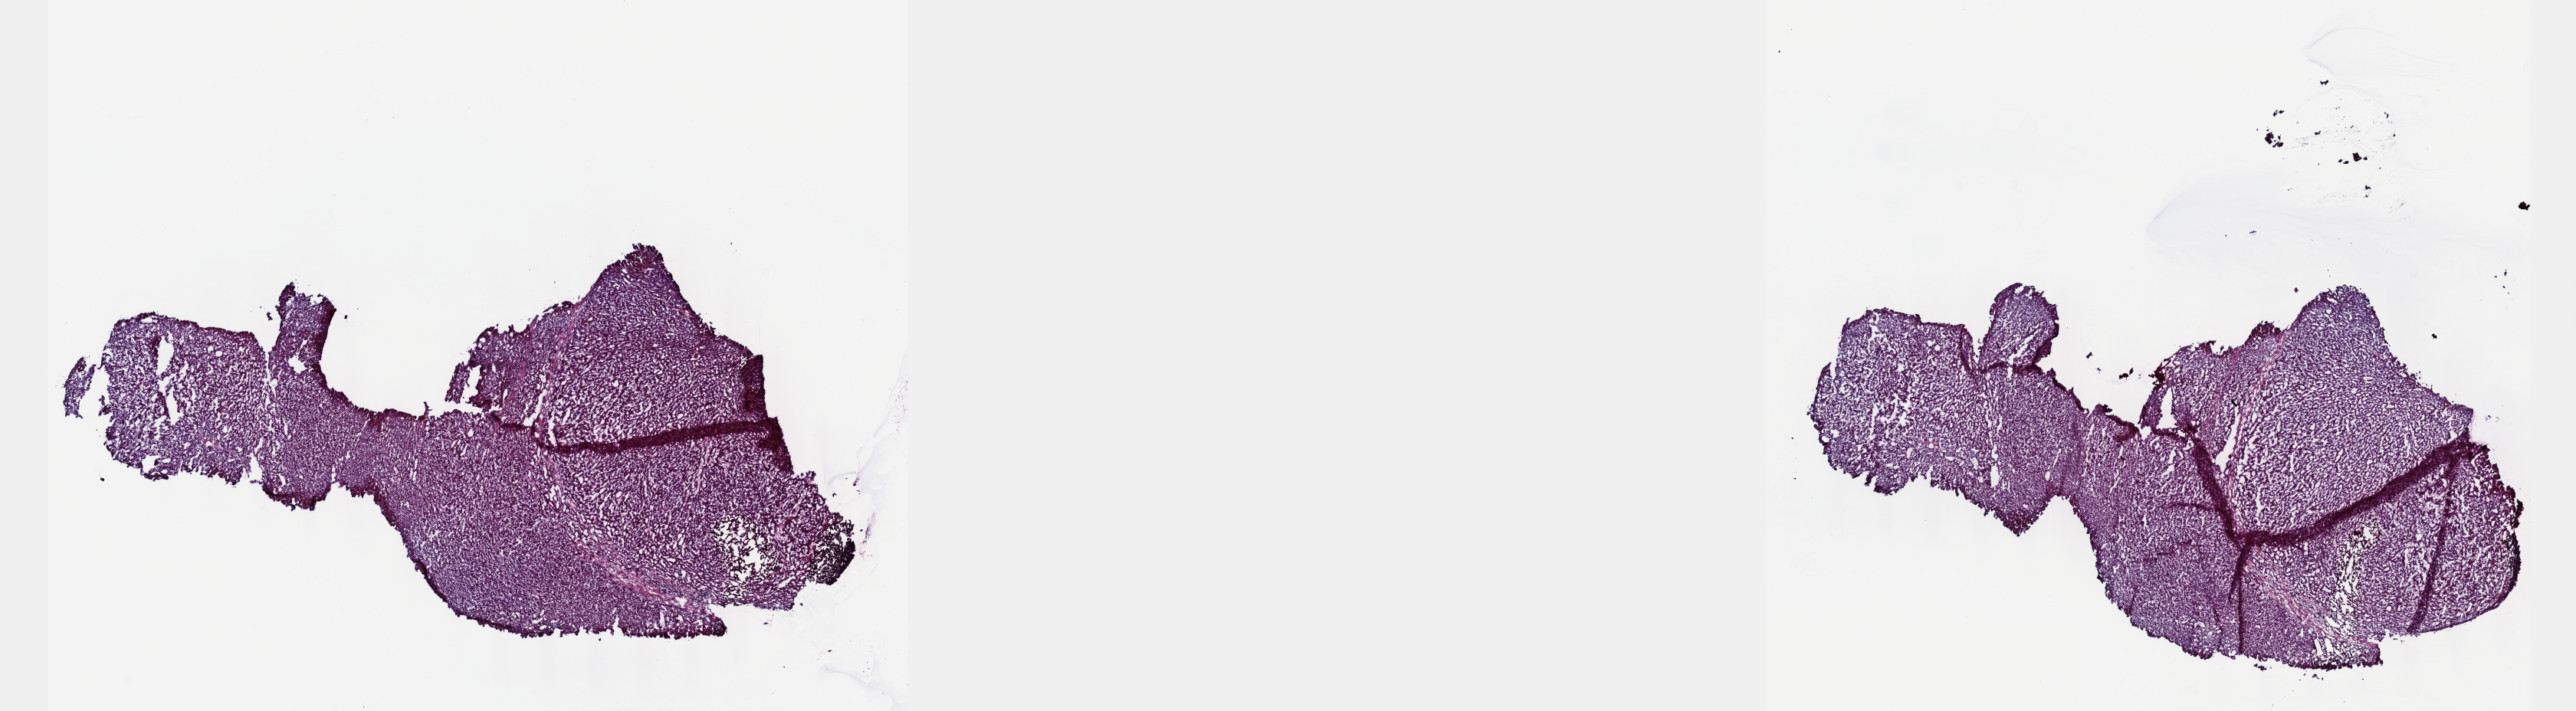
H&E whole-slide image — shown as a low-resolution overview of the whole scanned area (about 27.2 x 7.5 mm, slide scanned at 40x), frozen section from the top of the tissue portion, primary tumour sample from the liver. Male patient; age at initial diagnosis 48 years. Histologic grade: G2 (moderately differentiated). Slide review estimates, as recorded: tumour cells 85%, tumour nuclei 85%, normal cells 0%, stromal cells 15%, necrosis 0%. Infiltration values recorded for this section: lymphocyte infiltration 3%, monocyte infiltration 1%, neutrophil infiltration 2%.
Diagnosis: Hepatocellular carcinoma, NOS. AJCC pathologic stage: I (7th edition).